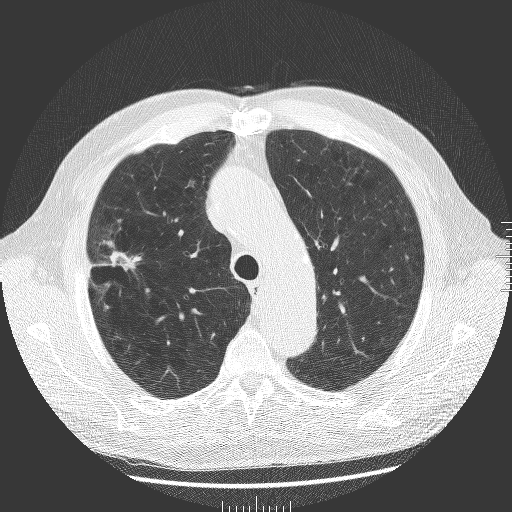
Low-dose screening chest CT, one axial slice. Position 140 of 181 along the scan axis. Reconstruction kernel BONE. 120 kVp. Lung window (W 1500 / L -600 HU). 2 mm slice thickness. 512 × 512 image matrix, field of view 380 × 380 mm.
Outlined on this slice (outlined manually by an expert reader):
- lesion 1 (tumor, upper lobe of right lung): bounding box [x1, y1, x2, y2] px = [110, 251, 141, 270]